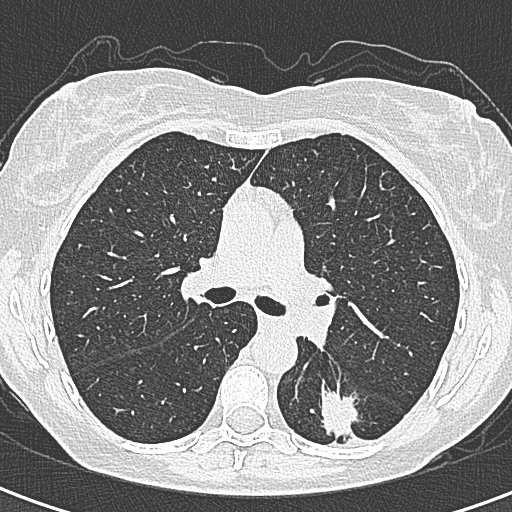
Low-dose screening chest CT, axial slice. First (baseline) screen. Lung window (W 1500 / L -600 HU). 1 mm slice thickness. Slice 123 of 328 in the series. Female participant, aged 58 years at enrolment.
Expert-annotated lung lesion, bounding box [x1, y1, x2, y2] px = [292, 389, 362, 454]. The screening reader recorded 2 non-calcified nodules or masses ≥4 mm on this exam (left lower lobe, right lower lobe); which of them this box marks is not recorded.